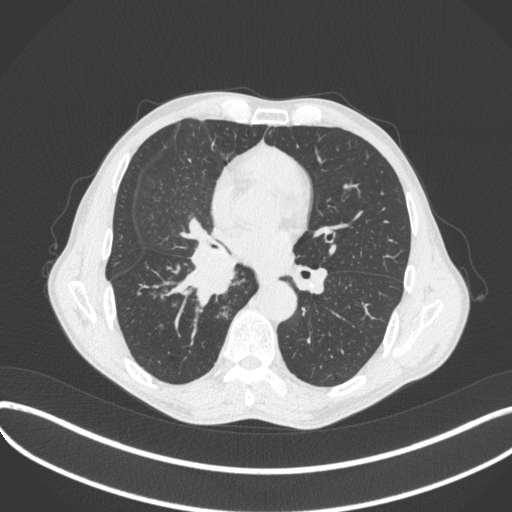
Chest CT, one axial slice. Slice 217 of 481 in the series (ordered by position). Lung window (W 1500 / L -600 HU). 1 mm slice thickness. 512 × 512 image matrix, field of view 400 × 400 mm. Male patient, age 65 years. From the clinical record (not read from this slice): clinical TNM (as recorded): T2a N0 M0.
Outlined on this slice (bounding box drawn by a radiologist):
- lung tumour (recorded histology: squamous cell carcinoma): bounding box (x1, y1, x2, y2) in pixels: (160, 237, 240, 308)